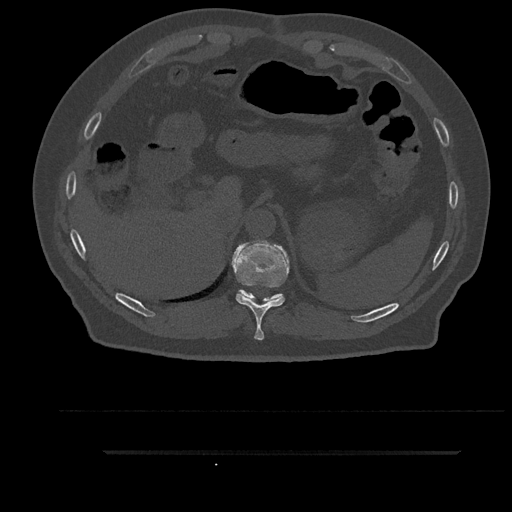
CT including the spine, one axial slice. Position 345 of 797 along the scan axis. 120 kVp. Bone window (W 1800 / L 400 HU). 0.5 mm slice thickness. 512 × 512 image matrix, field of view 432 × 432 mm. Male patient, age 63 years. From the clinical record (not read from this slice): primary cancer: renal.
Annotated regions visible in this slice (semi-automatic segmentation, software-assisted and operator-edited):
- T10 vertebra: bounding box [x1, y1, x2, y2] px = [232, 241, 289, 341]
- T11 vertebra: [237, 290, 282, 301]